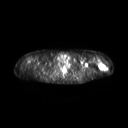
FDG PET of an extremity soft-tissue mass (from a PET/CT study), one axial slice. Position 206 of 267 along the scan axis. 3.27 mm slice thickness. 128 × 128 image matrix, field of view 600 × 600 mm. Patient: female, 28 years. From the clinical record (not read from this slice): histological type: malignant fibrous histiocytoma; grade: low; site of the primary tumour: left arm.
Annotated regions visible in this slice (expert contour drawn on MRI and transferred to this co-registered scan by the dataset authors):
- gross tumour volume (mass): bounding box [x1, y1, x2, y2] px = [98, 62, 107, 70]